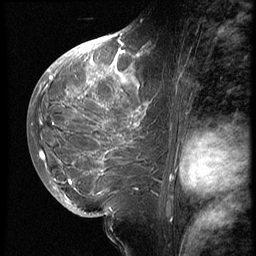
Breast MRI (dynamic contrast-enhanced), one sagittal slice; 3 images stored at this slice position (order not interpretable as contrast timing); 1.5 T; TE 4.2 ms, TR 9 ms; 256 × 256 image matrix. Patient: female, 28 years. Case-level facts recorded for this patient, not image findings: setting: breast cancer imaged before/during neoadjuvant chemotherapy.
Annotated regions visible in this slice (semi-automatically segmented with operator editing):
- analysis volume of interest (the breast-tissue region the enhancement analysis was run in; not a lesion): bounding box (x1, y1, x2, y2) in pixels: (42, 45, 163, 207)
- tumour enhancement mask (voxels above the 140 % enhancement threshold inside the analysis volume of interest): (42, 46, 146, 195)